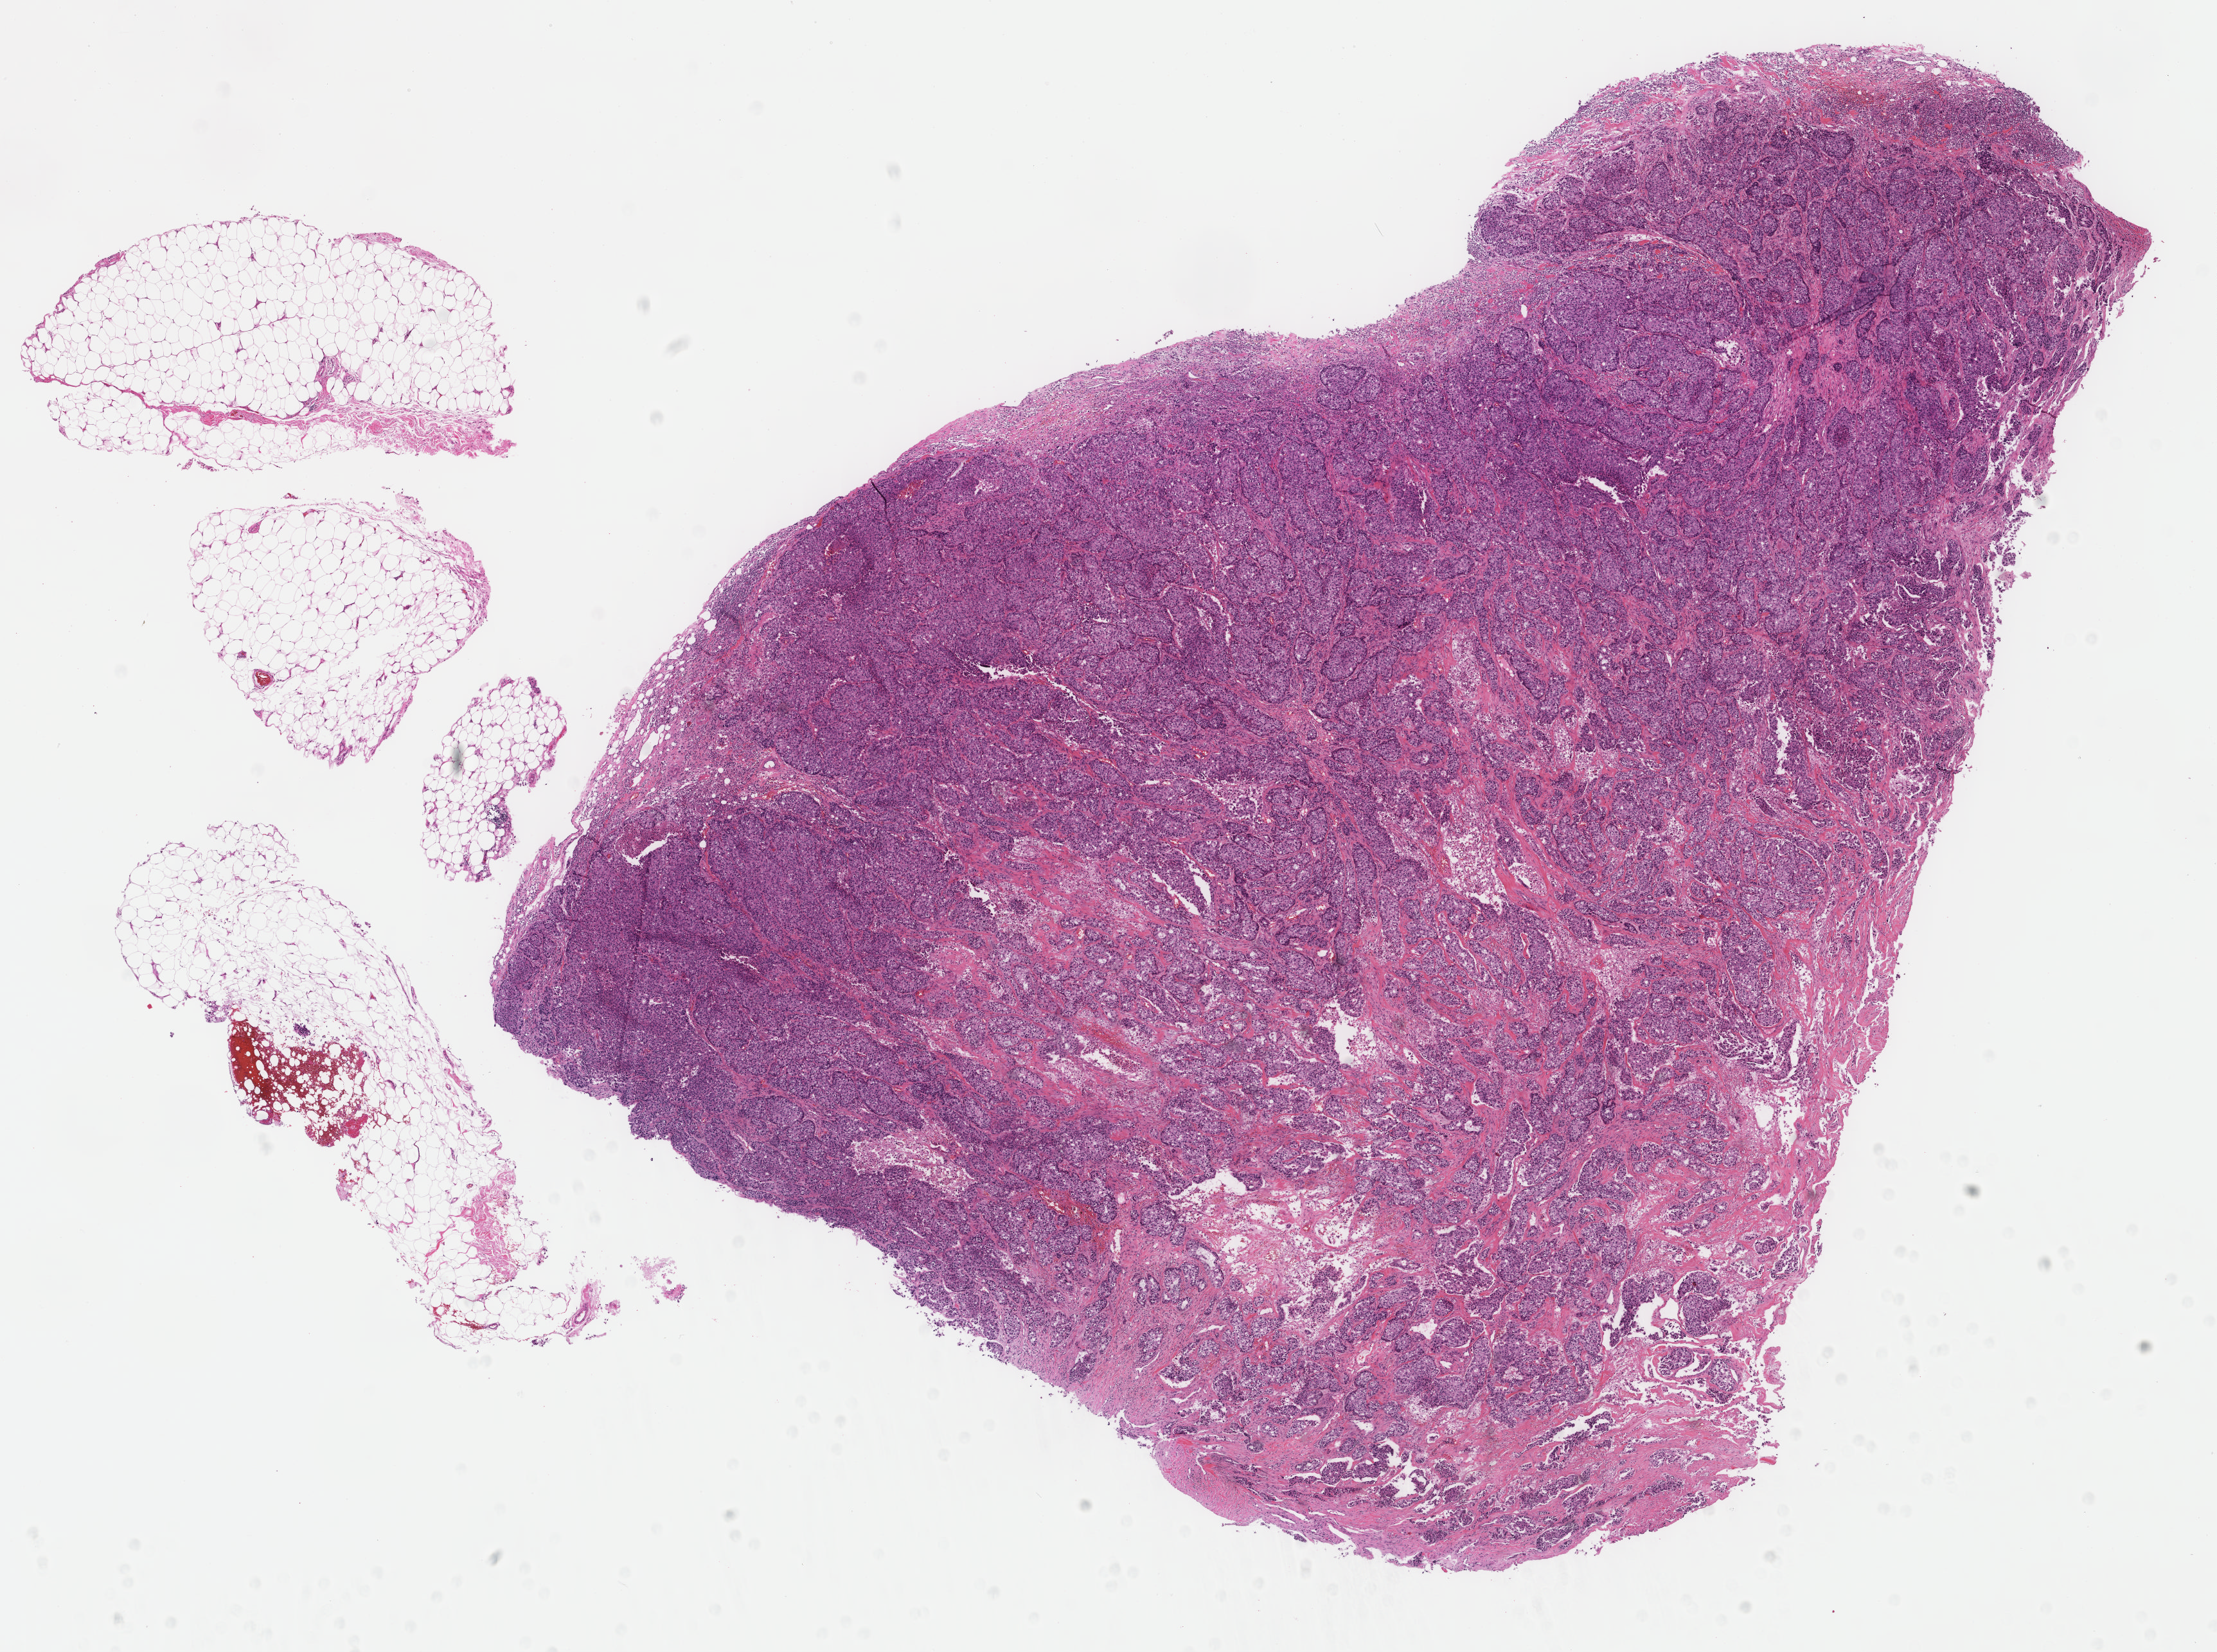
Digitized Hematoxylin and eosin (H&E) stained tissue section (whole slide), low-resolution overview of the scanned area, about 13.7 x 10.2 mm (acquisition: 40x scan), formalin-fixed paraffin-embedded (FFPE) diagnostic section, primary tumour sample from the breast. Female patient; age at initial diagnosis 56 years.
AJCC pathologic stage: IIA. Lymph nodes positive (case pathology): 0 of 23 examined. Laterality: right. Pathologic diagnosis: Infiltrating duct carcinoma, NOS.